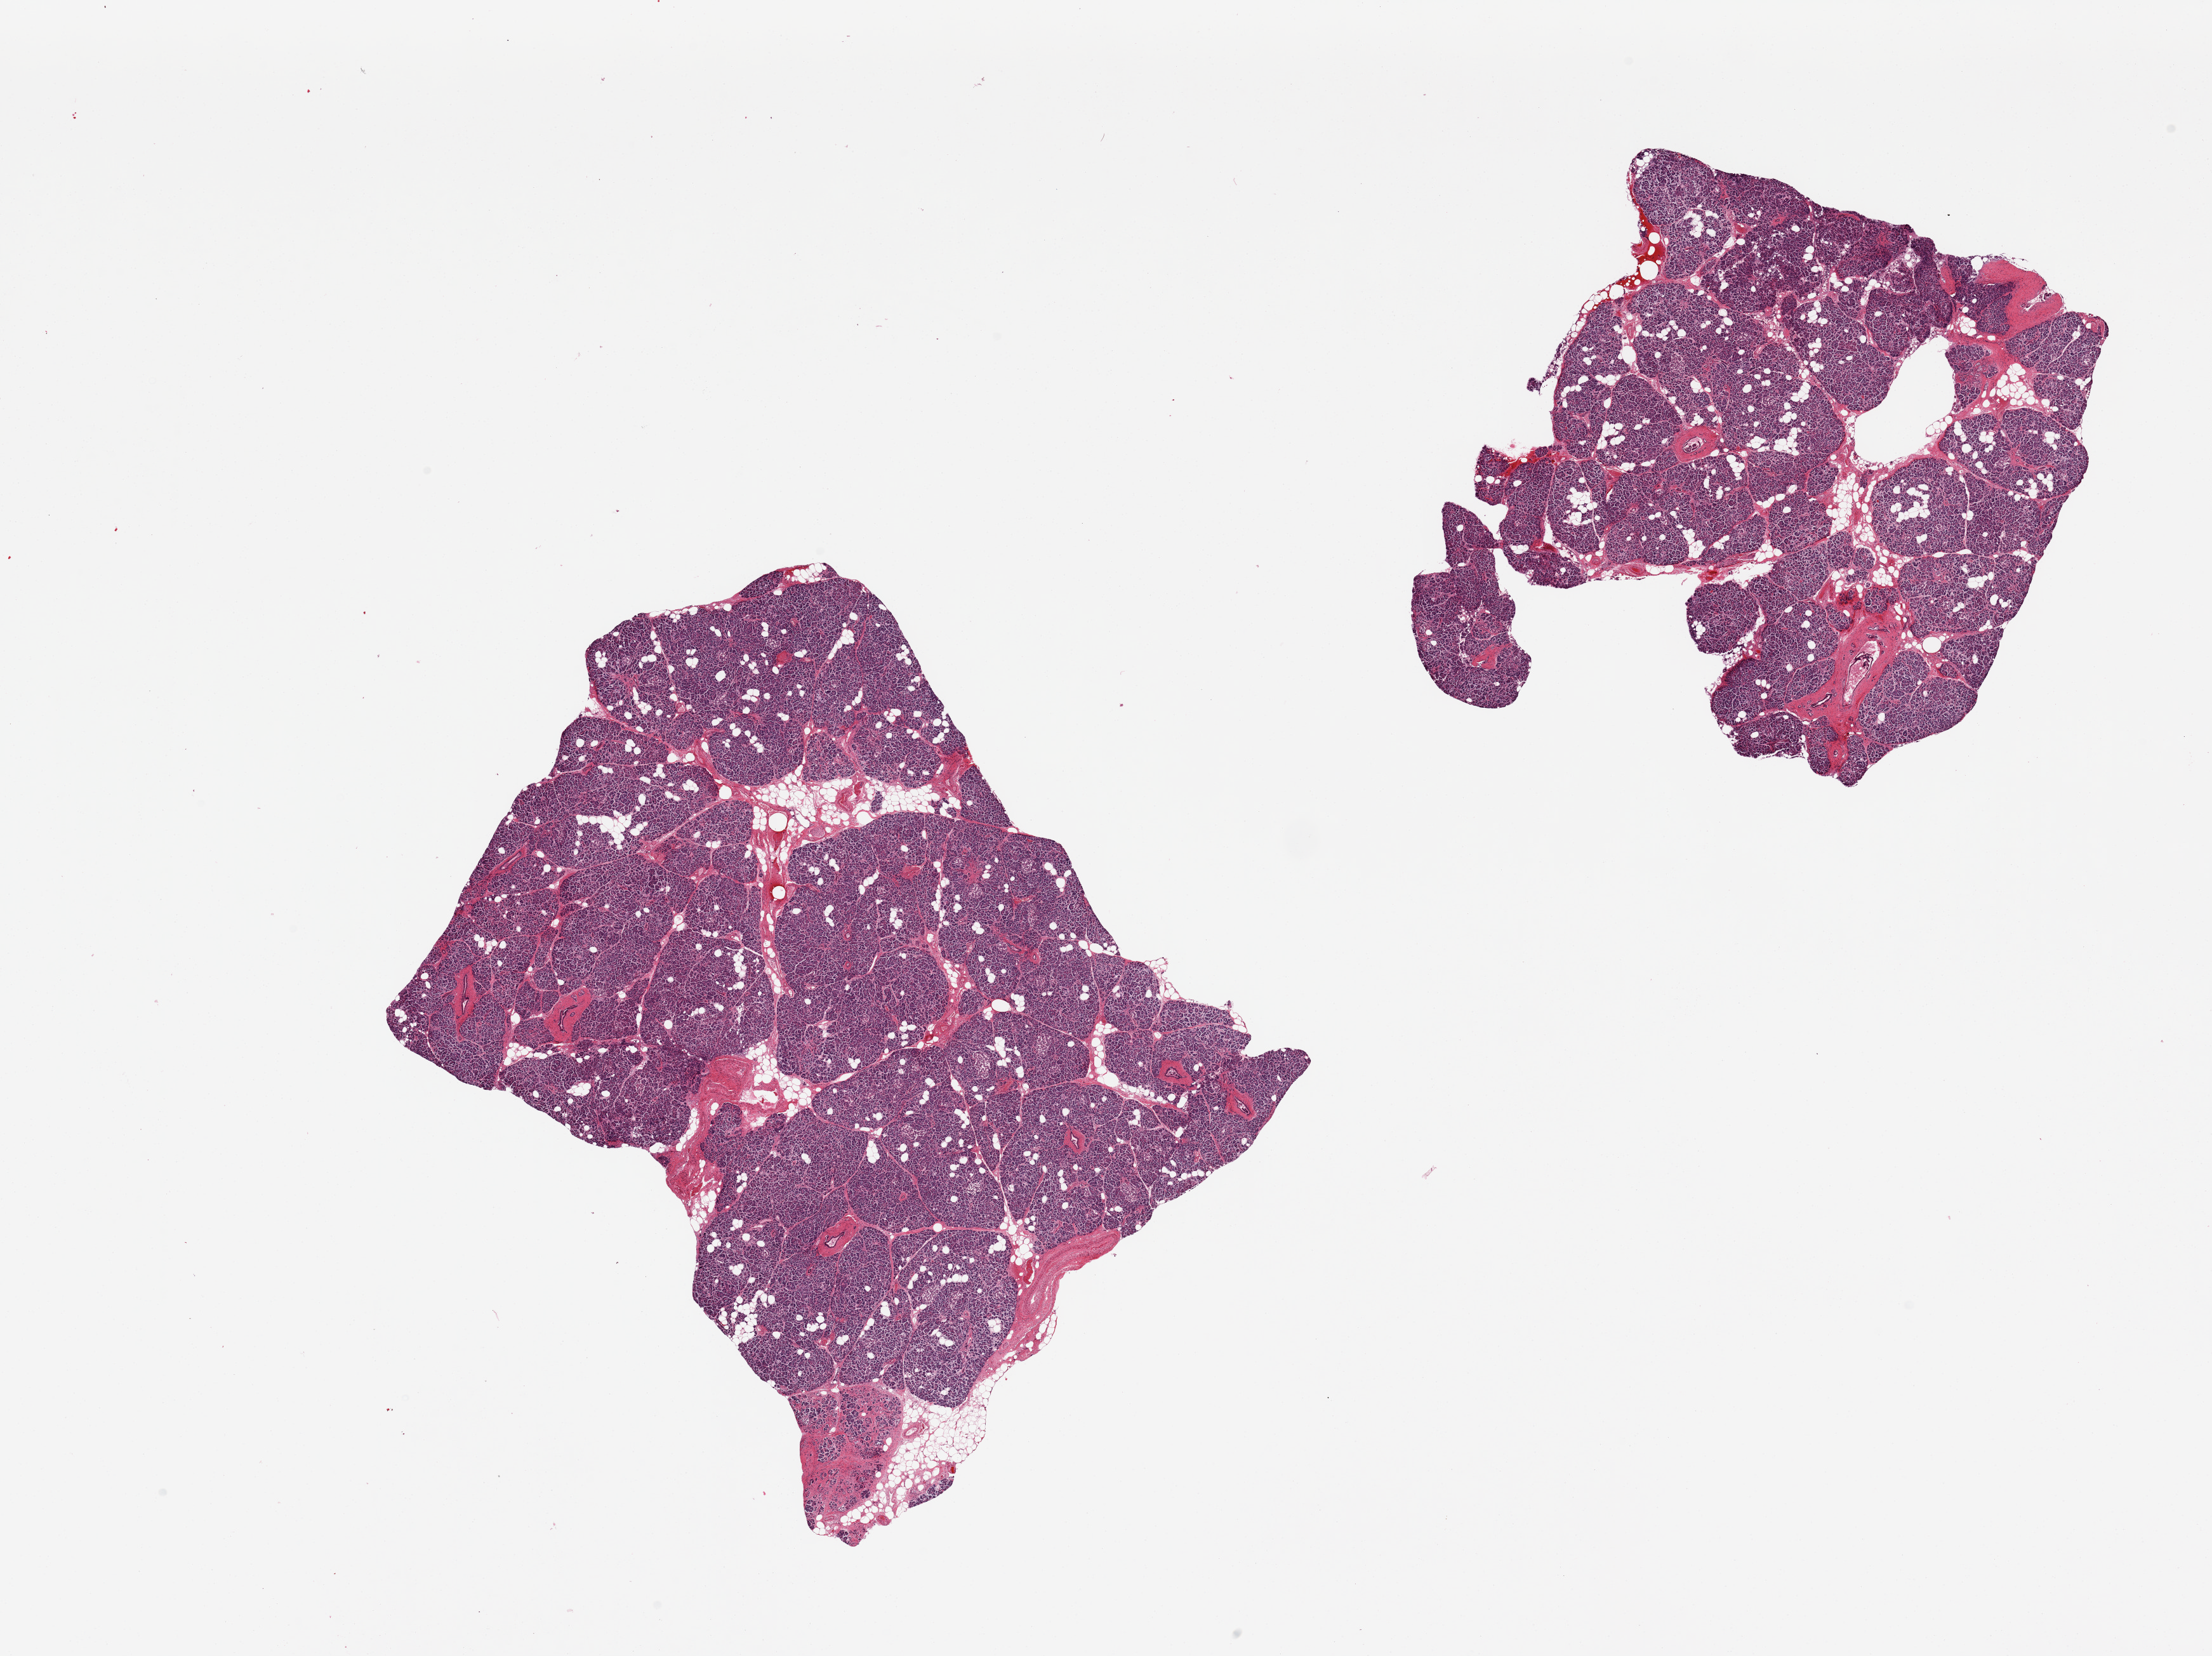
Digitized H&E-stained section, brightfield, shown as a low-resolution overview of the whole scanned area (about 27.6 x 20.6 mm, acquisition: 20x scan). PAXgene-fixed paraffin-embedded (PFPE) section. Section of pancreas (target tissue). Donor tissue sample.
Reviewer comment on this tissue sample: 2 pieces, focal atrophy and fibrosis, interstitial fibrosis.